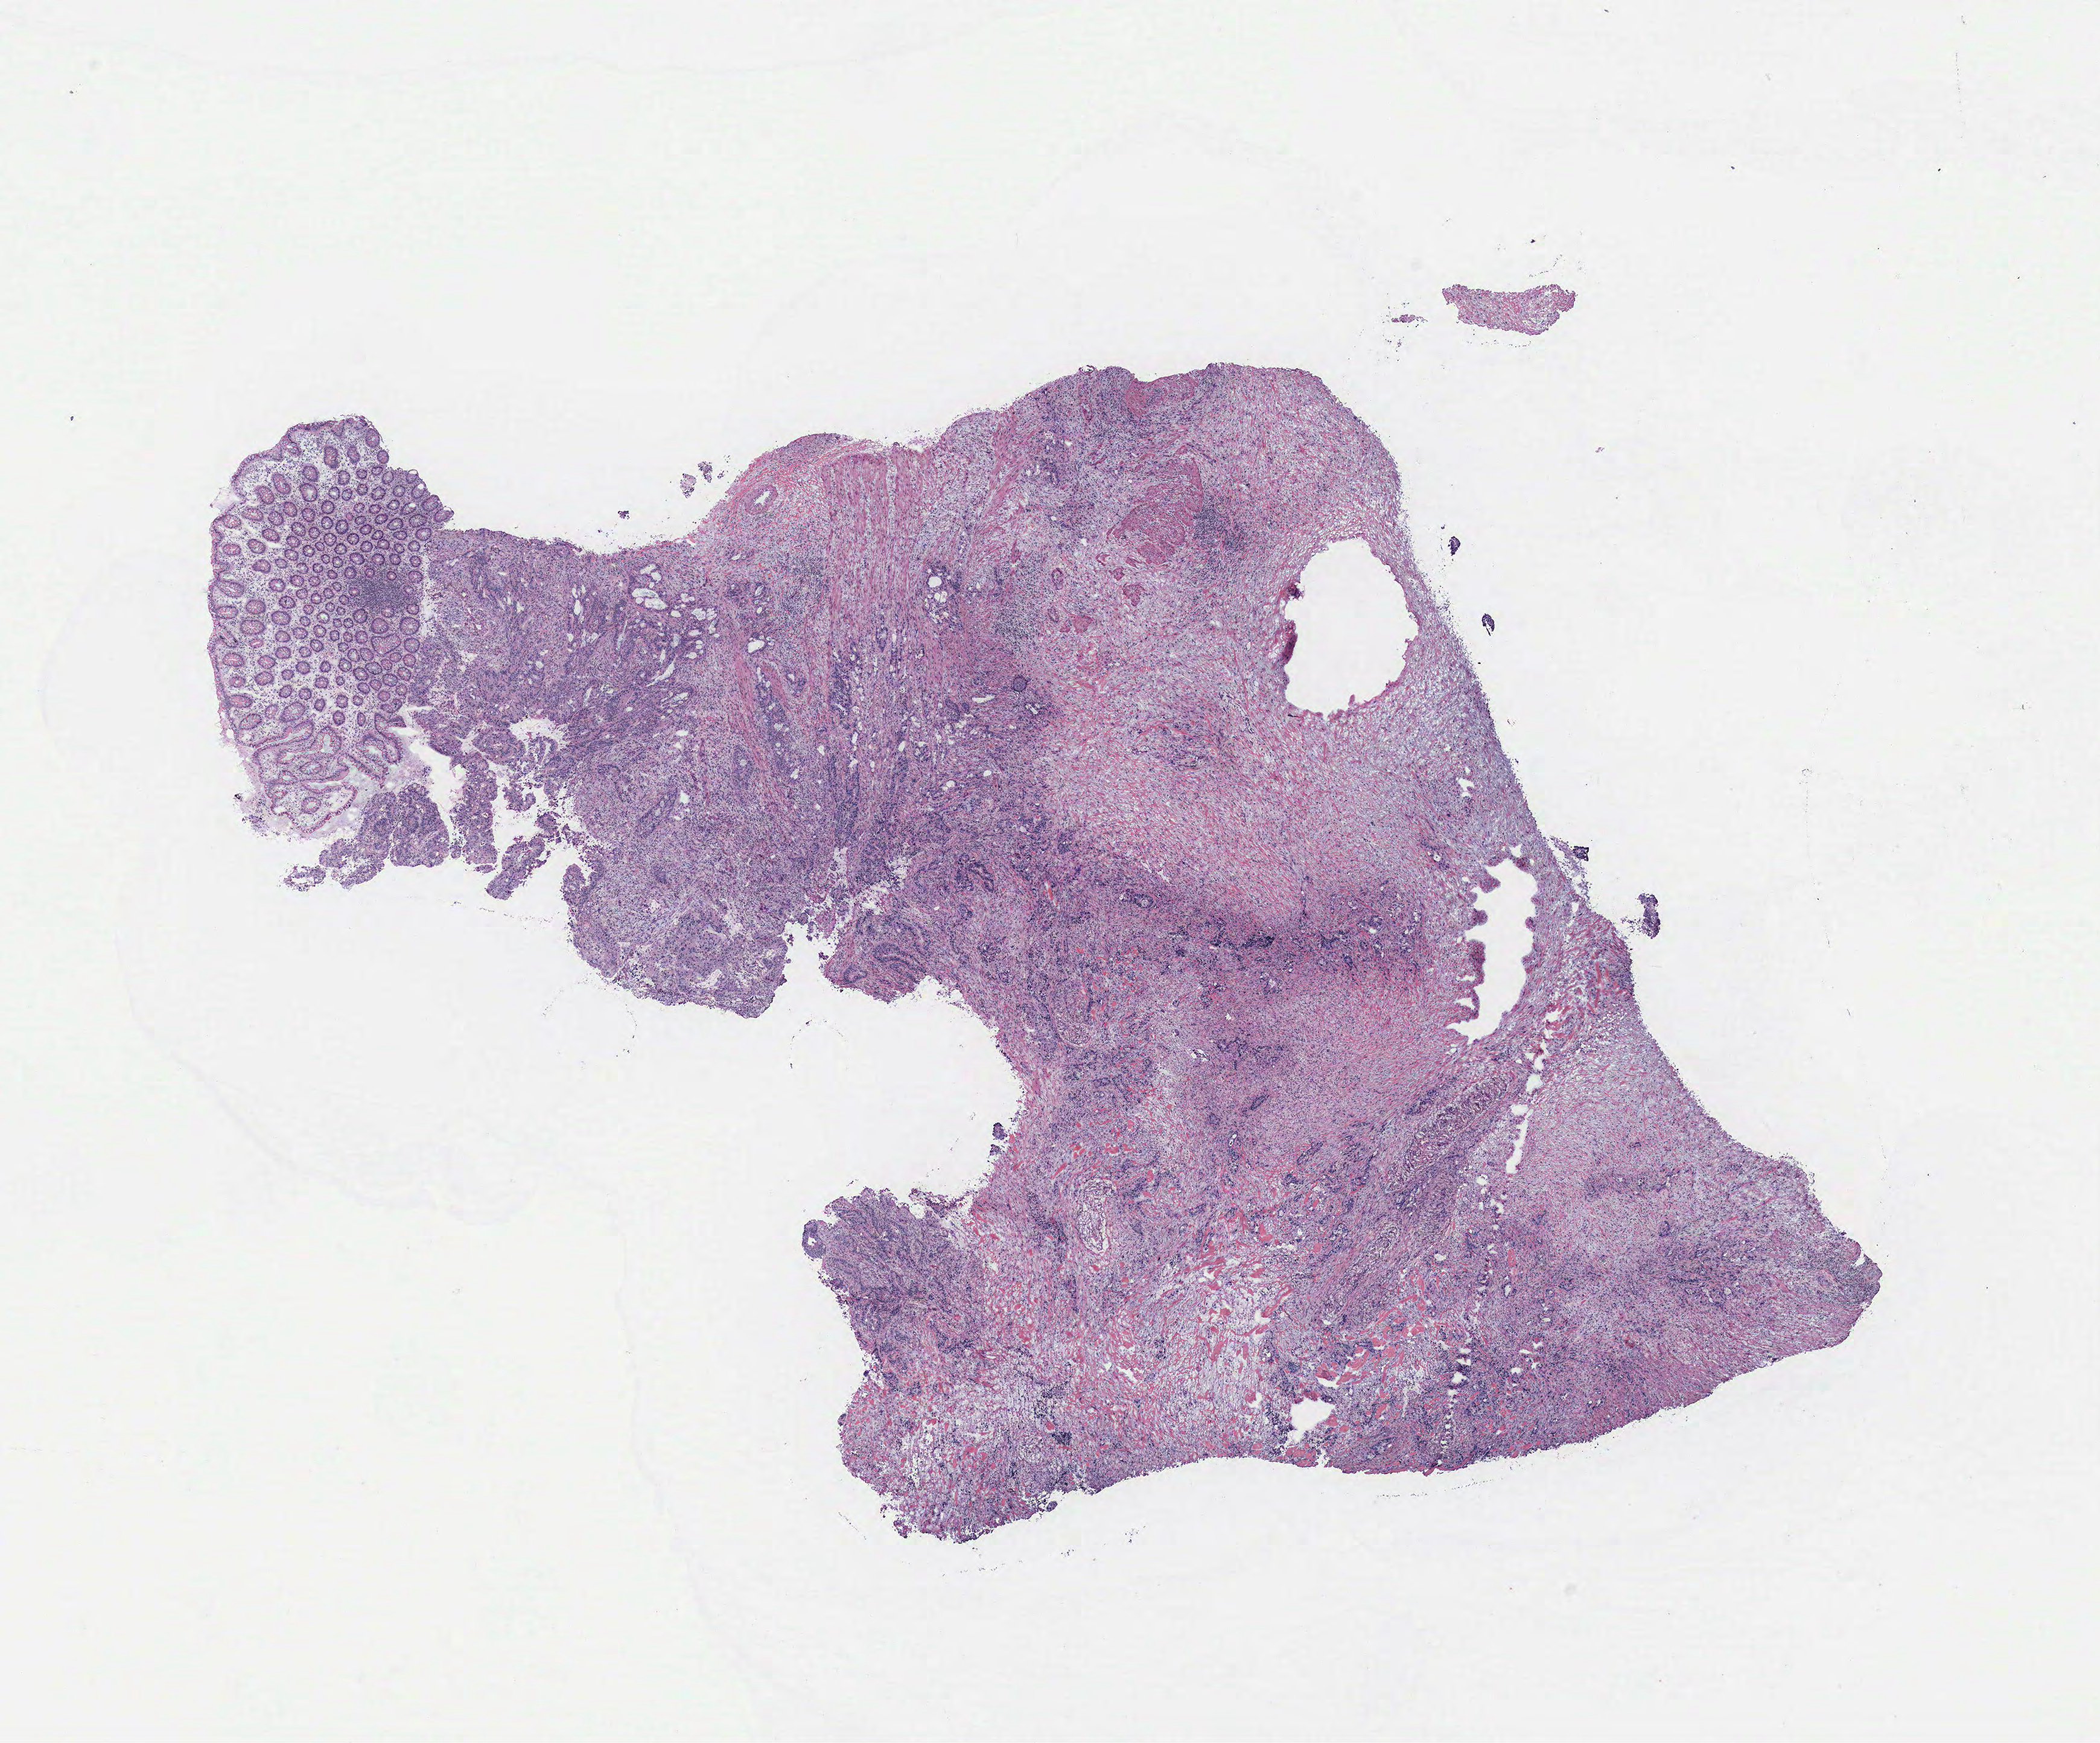
H&E whole-slide image — whole scanned area (about 13.9 x 11.6 mm) shown as a low-resolution overview. Colon, tissue type not recorded. Female patient.
* patient diagnosis: Adenocarcinoma, NOS